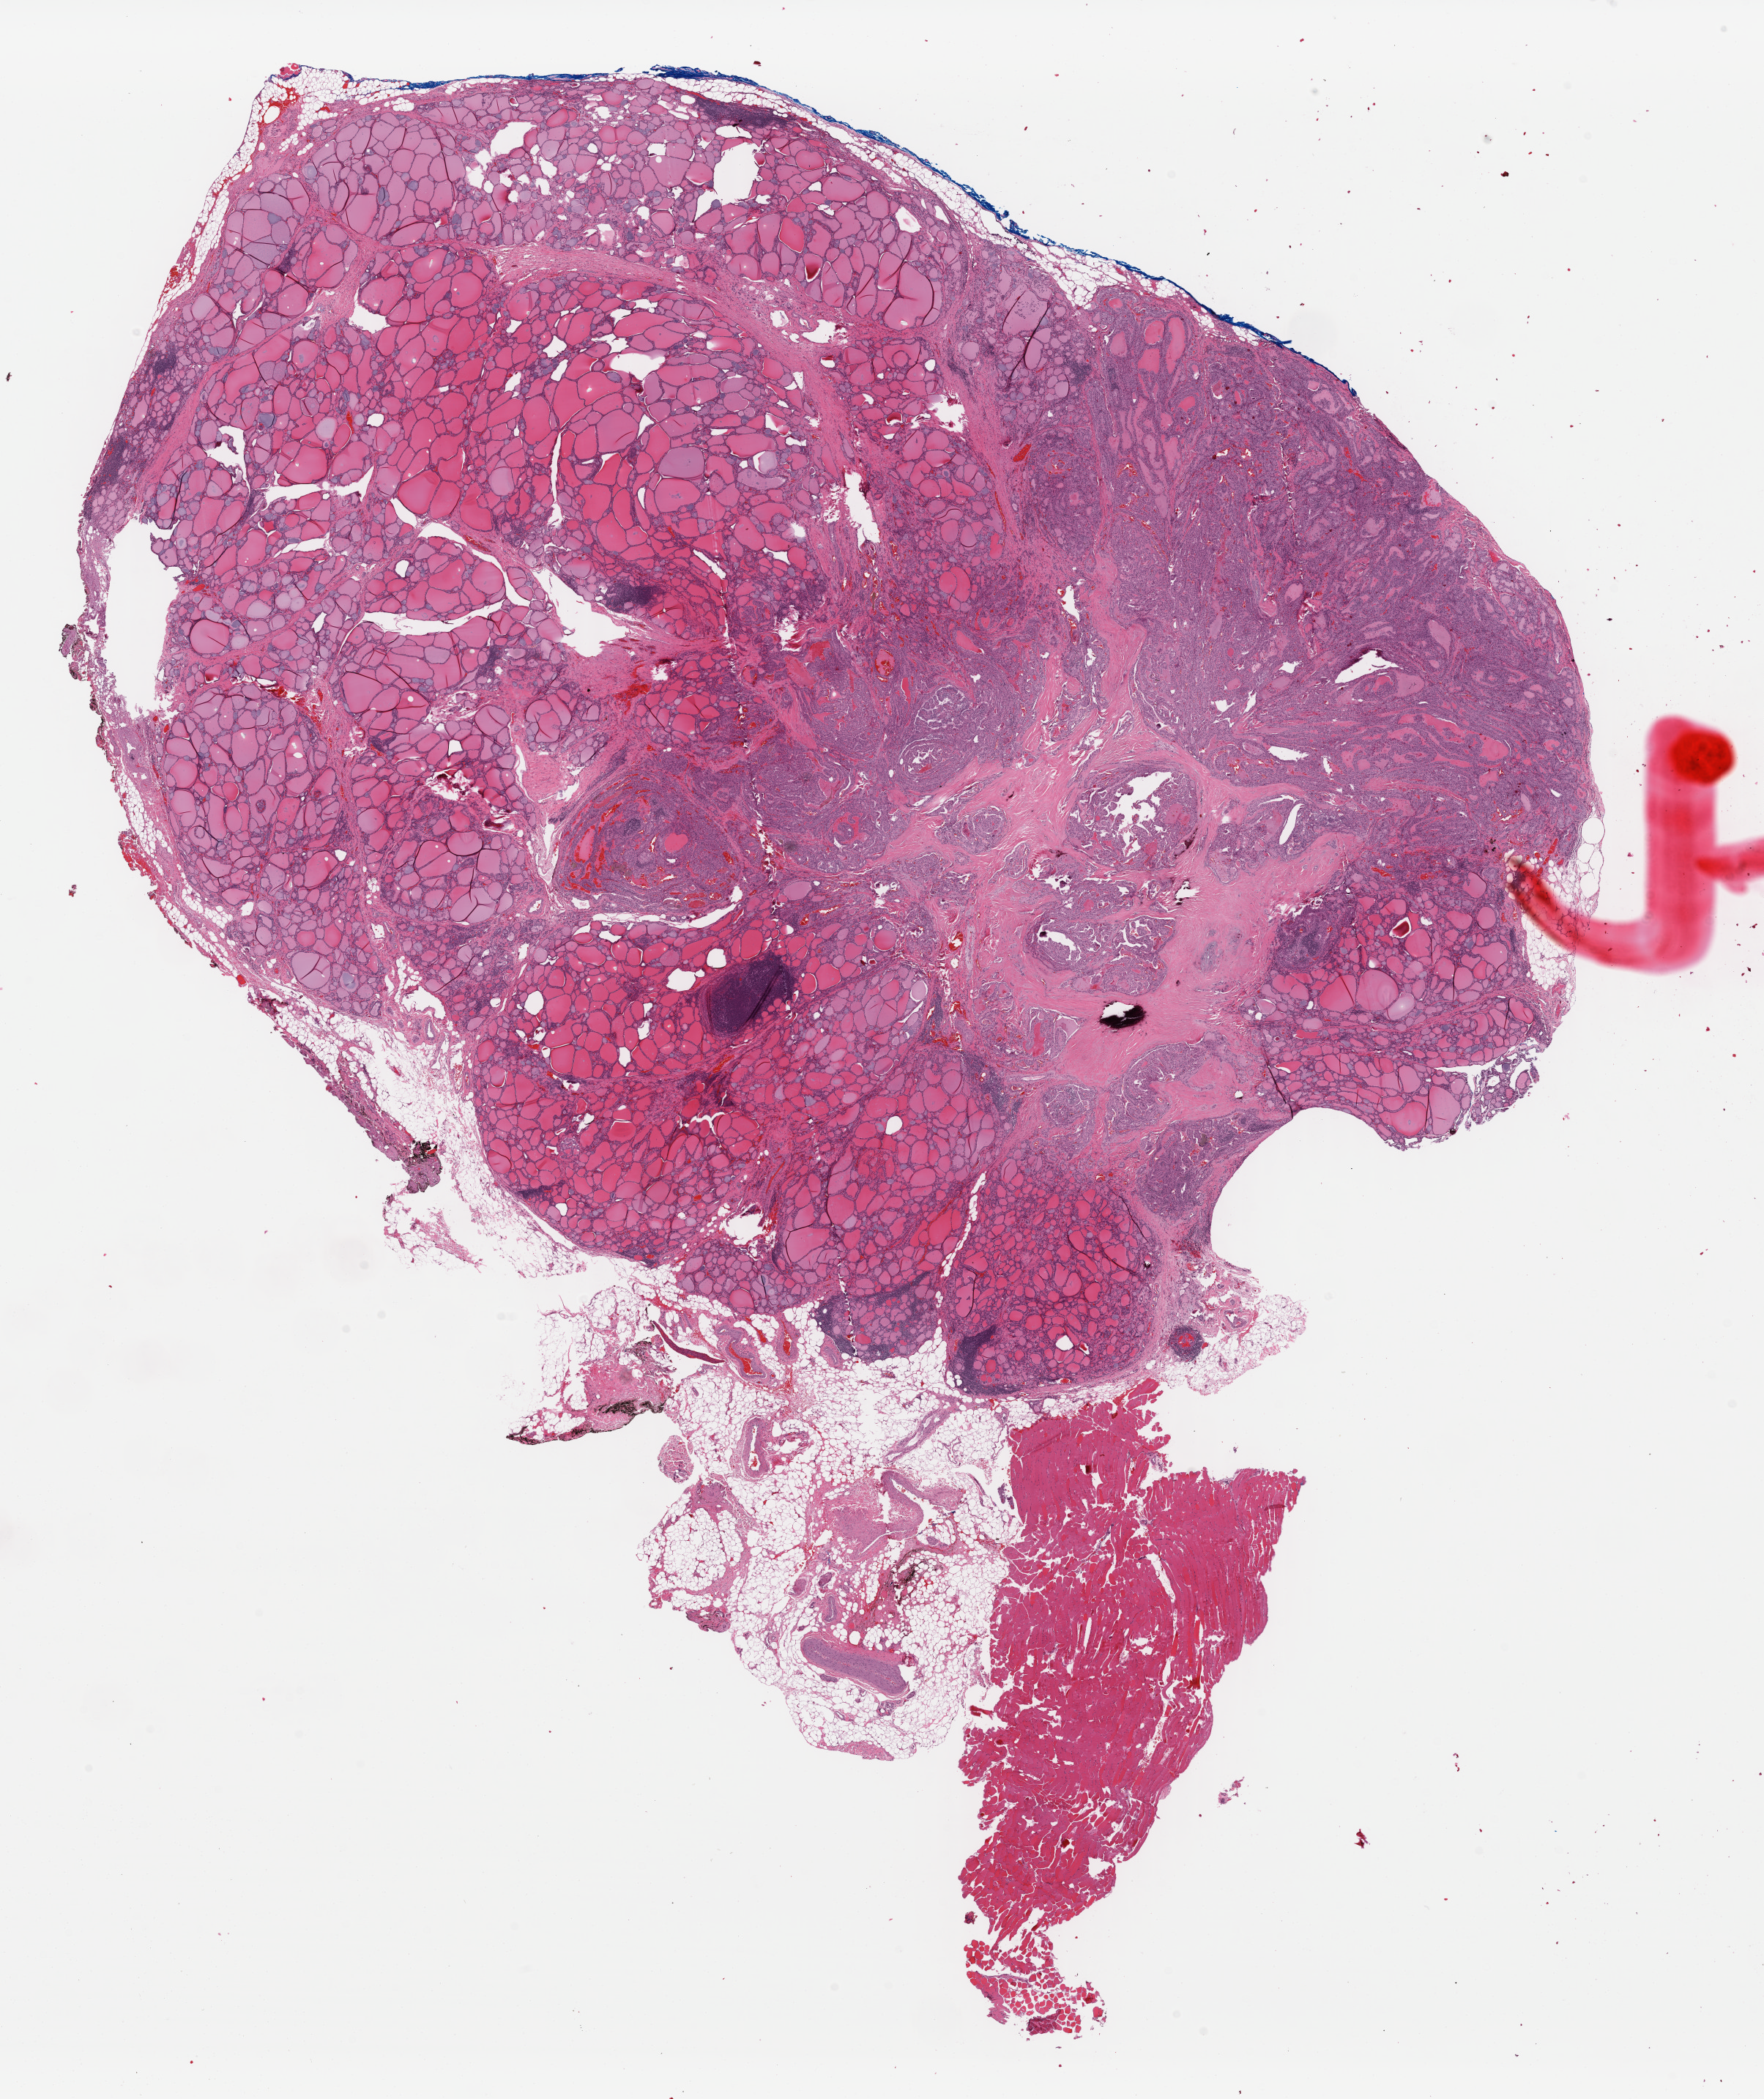
H&E whole-slide image — shown as a low-resolution overview of the whole scanned area (about 19.0 x 22.6 mm, slide scanned at 40x), formalin-fixed paraffin-embedded (FFPE) diagnostic section, sample: primary tumour, thyroid. Male patient; age at initial diagnosis 56 years.
AJCC pathologic stage: IVA. Pathologic diagnosis: Papillary carcinoma, columnar cell (thyroid gland).